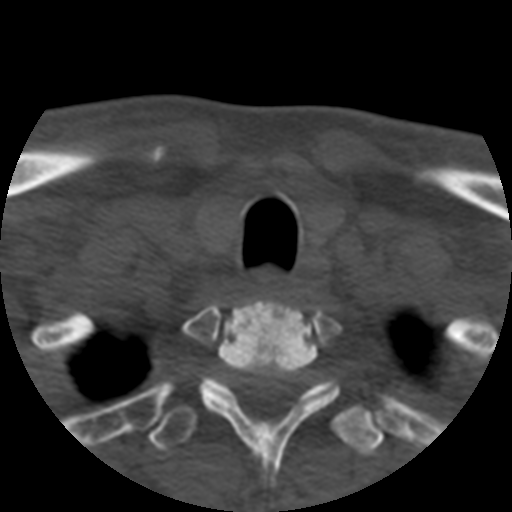
CT including the spine, one axial slice; slice 443 of 508 in the series (ordered by position); 120 kVp; bone window (W 1800 / L 400 HU); 1.25 mm slice thickness; 512 × 512 image matrix. Patient age 57 years. Case-level facts recorded for this patient, not image findings: primary cancer: prostate.
Structures marked on this image (semi-automatically segmented with operator editing):
- T1 vertebra: box from (x=164, y=299) to (x=339, y=469) px
- T2 vertebra: (x=147, y=378)–(x=384, y=455)